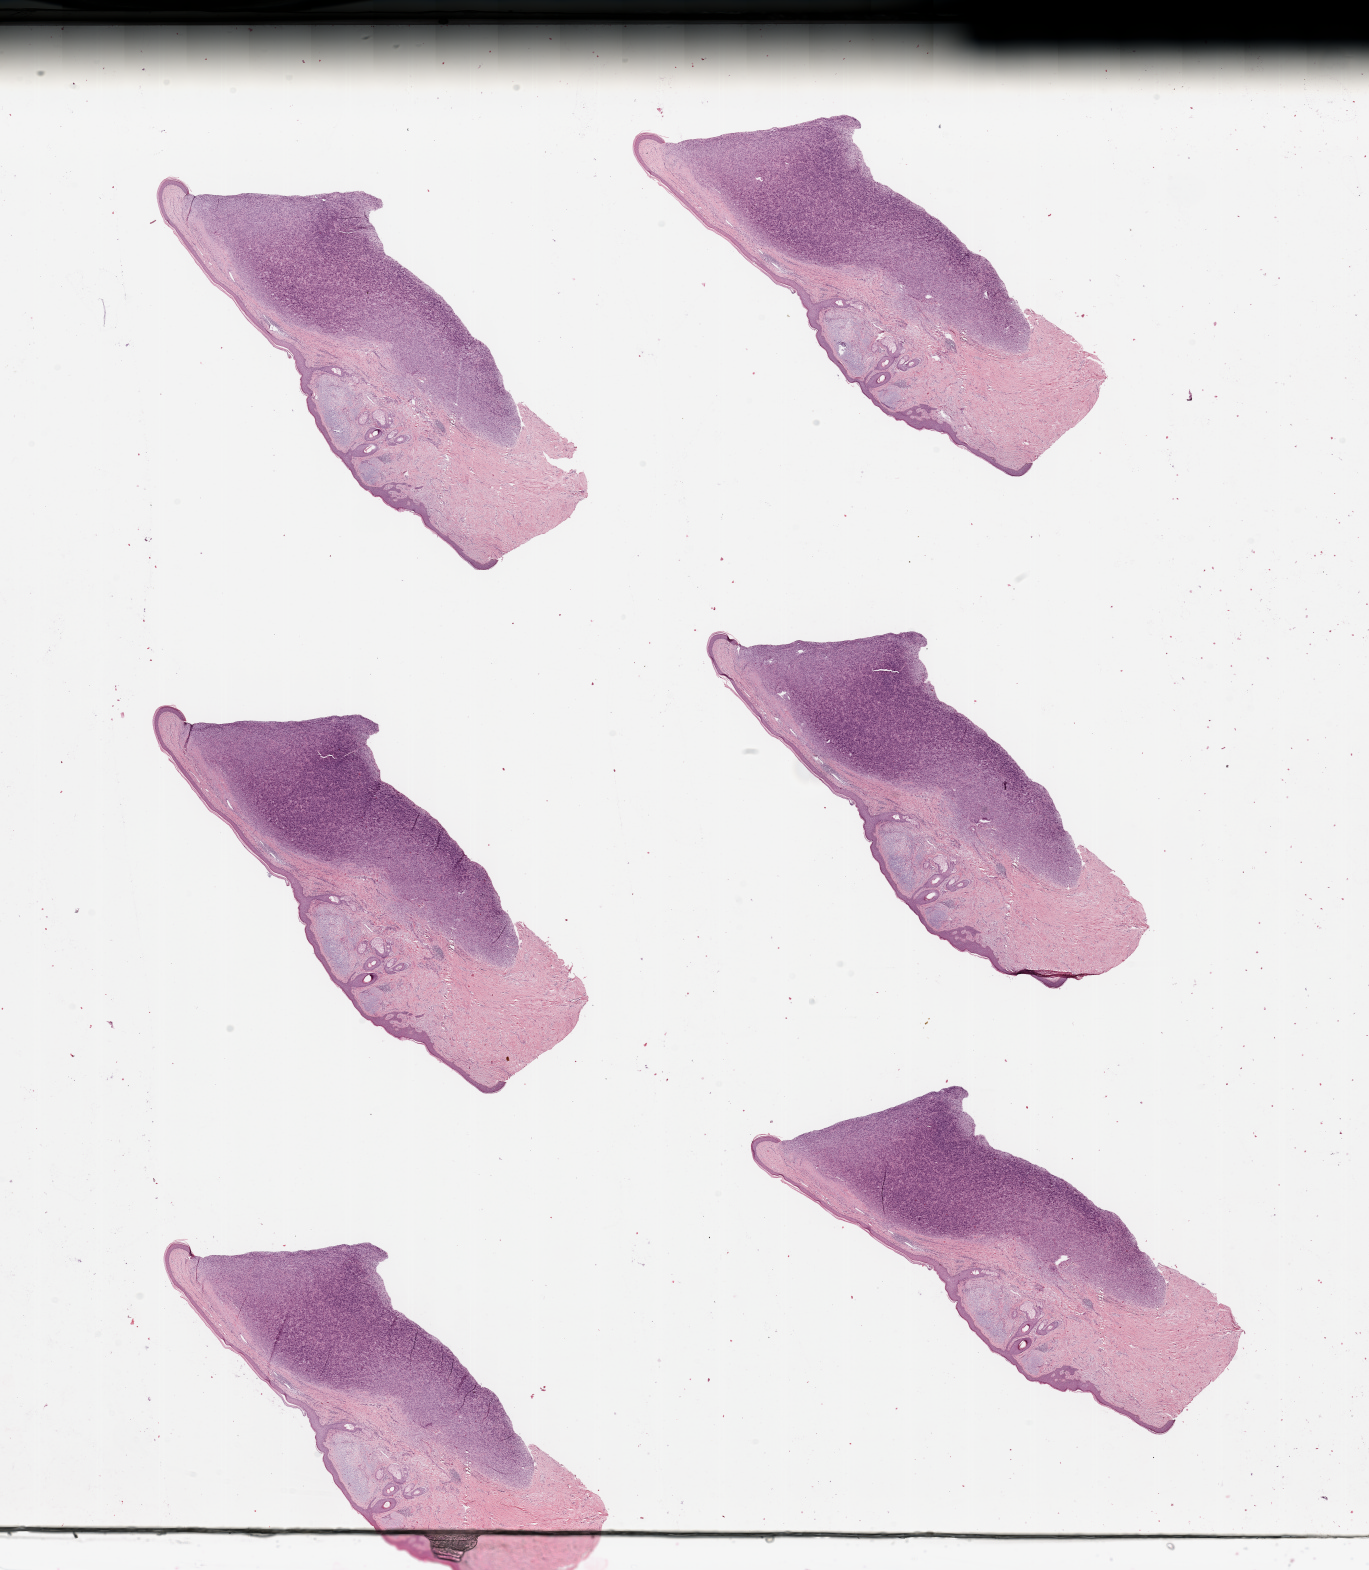
Whole-slide histology image, H&E-stained — a low-resolution overview of the entire scanned area, about 21.7 x 24.8 mm; tumour tissue sample. Male, 68 y/o.
Patient diagnosis (cohort enrolment): sarcoma (site not recorded at cohort level).